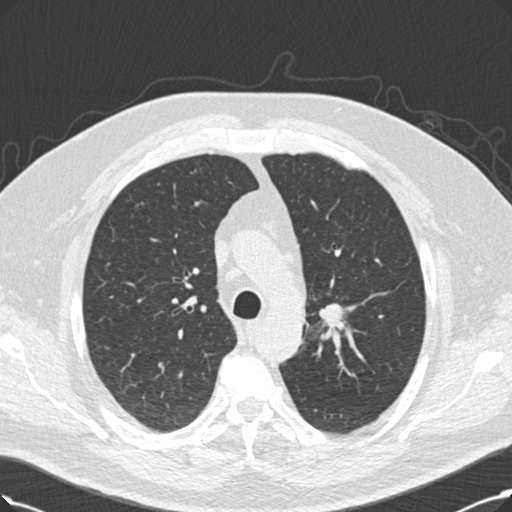
Low-dose screening chest CT, one axial slice; 120 kVp; lung window (W 1500 / L -600 HU); 2 mm slice thickness; 512 × 512 image matrix.
Annotated regions visible in this slice (outlined manually by an expert reader):
- lesion 1 (tumor): box from (x=319, y=304) to (x=348, y=329) px